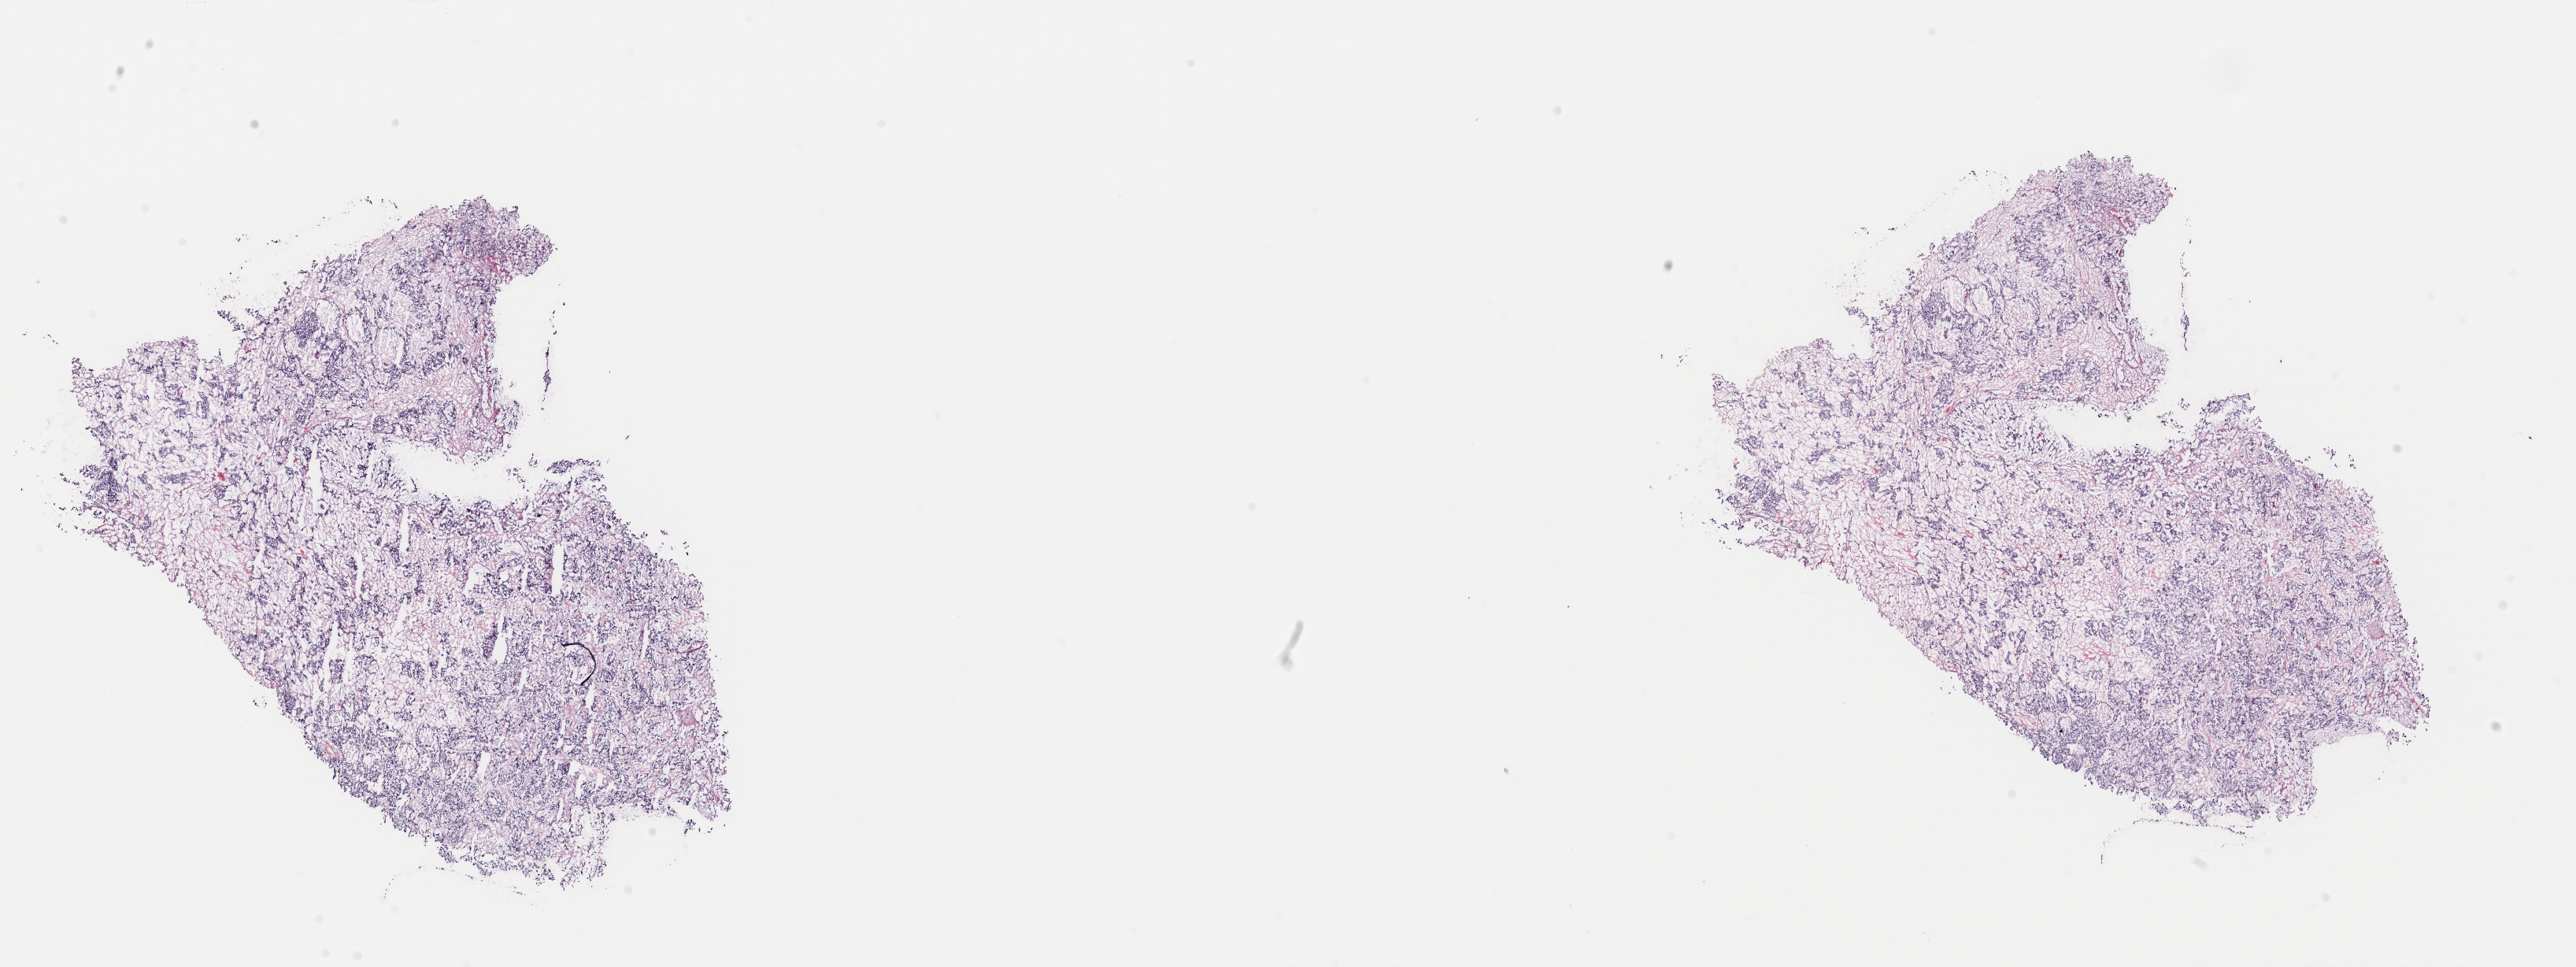
H&E-stained whole-slide image — whole scanned area (about 25.8 x 9.7 mm, from a 40x scan) shown as a low-resolution overview, frozen section from the top of the tissue portion, adrenal gland, primary tumour sample. Patient: female, age at initial diagnosis 51 years. Composition of this section per pathologist review: tumour cells 100%, tumour nuclei 75%, normal cells 0%, stromal cells 0%, necrosis 0%. Infiltration values recorded for this section: lymphocyte infiltration 1%, monocyte infiltration 0%, neutrophil infiltration 0%.
Diagnosis: Pheochromocytoma, NOS. Laterality: left.